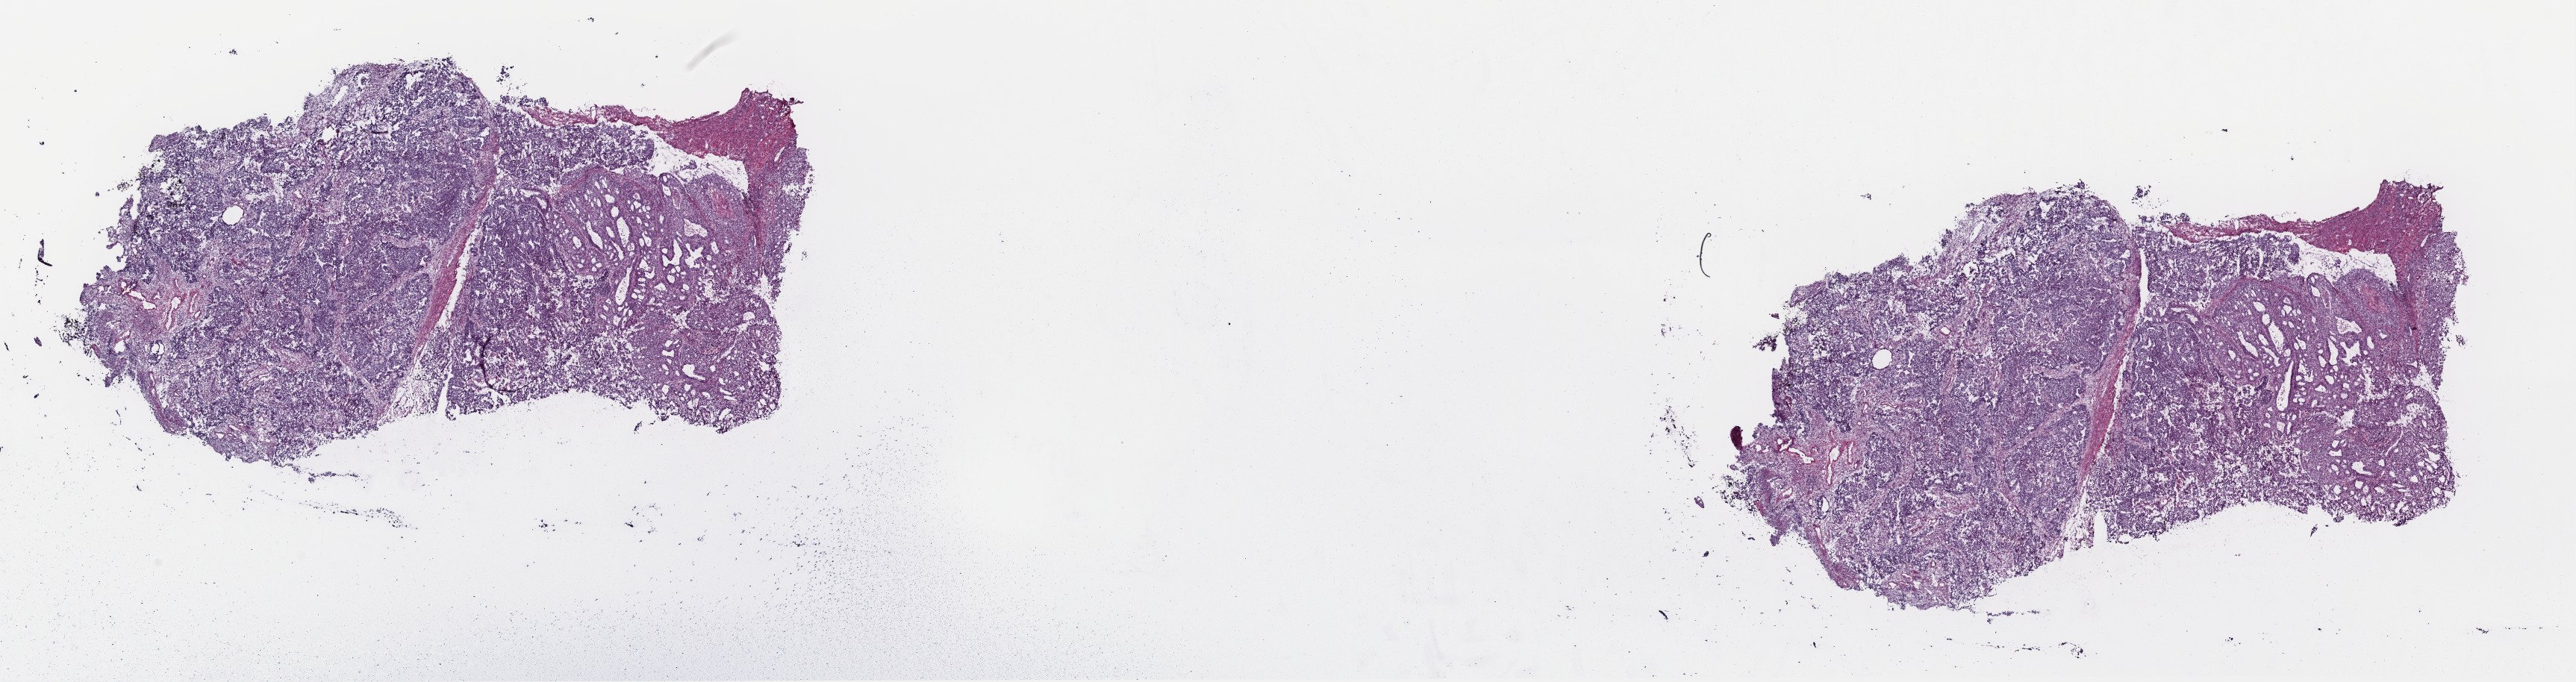
H&E whole-slide image, low-resolution overview of the scanned area, about 27.3 x 7.2 mm (acquisition: 40x scan), frozen section from the top of the tissue portion, uterus, primary tumour sample. Female, age 83 years at initial diagnosis. Histologic grade: G3 (poorly differentiated). Composition of this section per pathologist review: tumour cells 85%, tumour nuclei 90%, normal cells 13%, stromal cells 0%, necrosis 2%. Infiltration values recorded for this section: lymphocyte infiltration 2%, monocyte infiltration 0%, neutrophil infiltration 1%.
FIGO stage: II. Pathologic diagnosis: Serous cystadenocarcinoma, NOS (endometrium). Lymph nodes positive (case pathology): 0 of 7 examined.